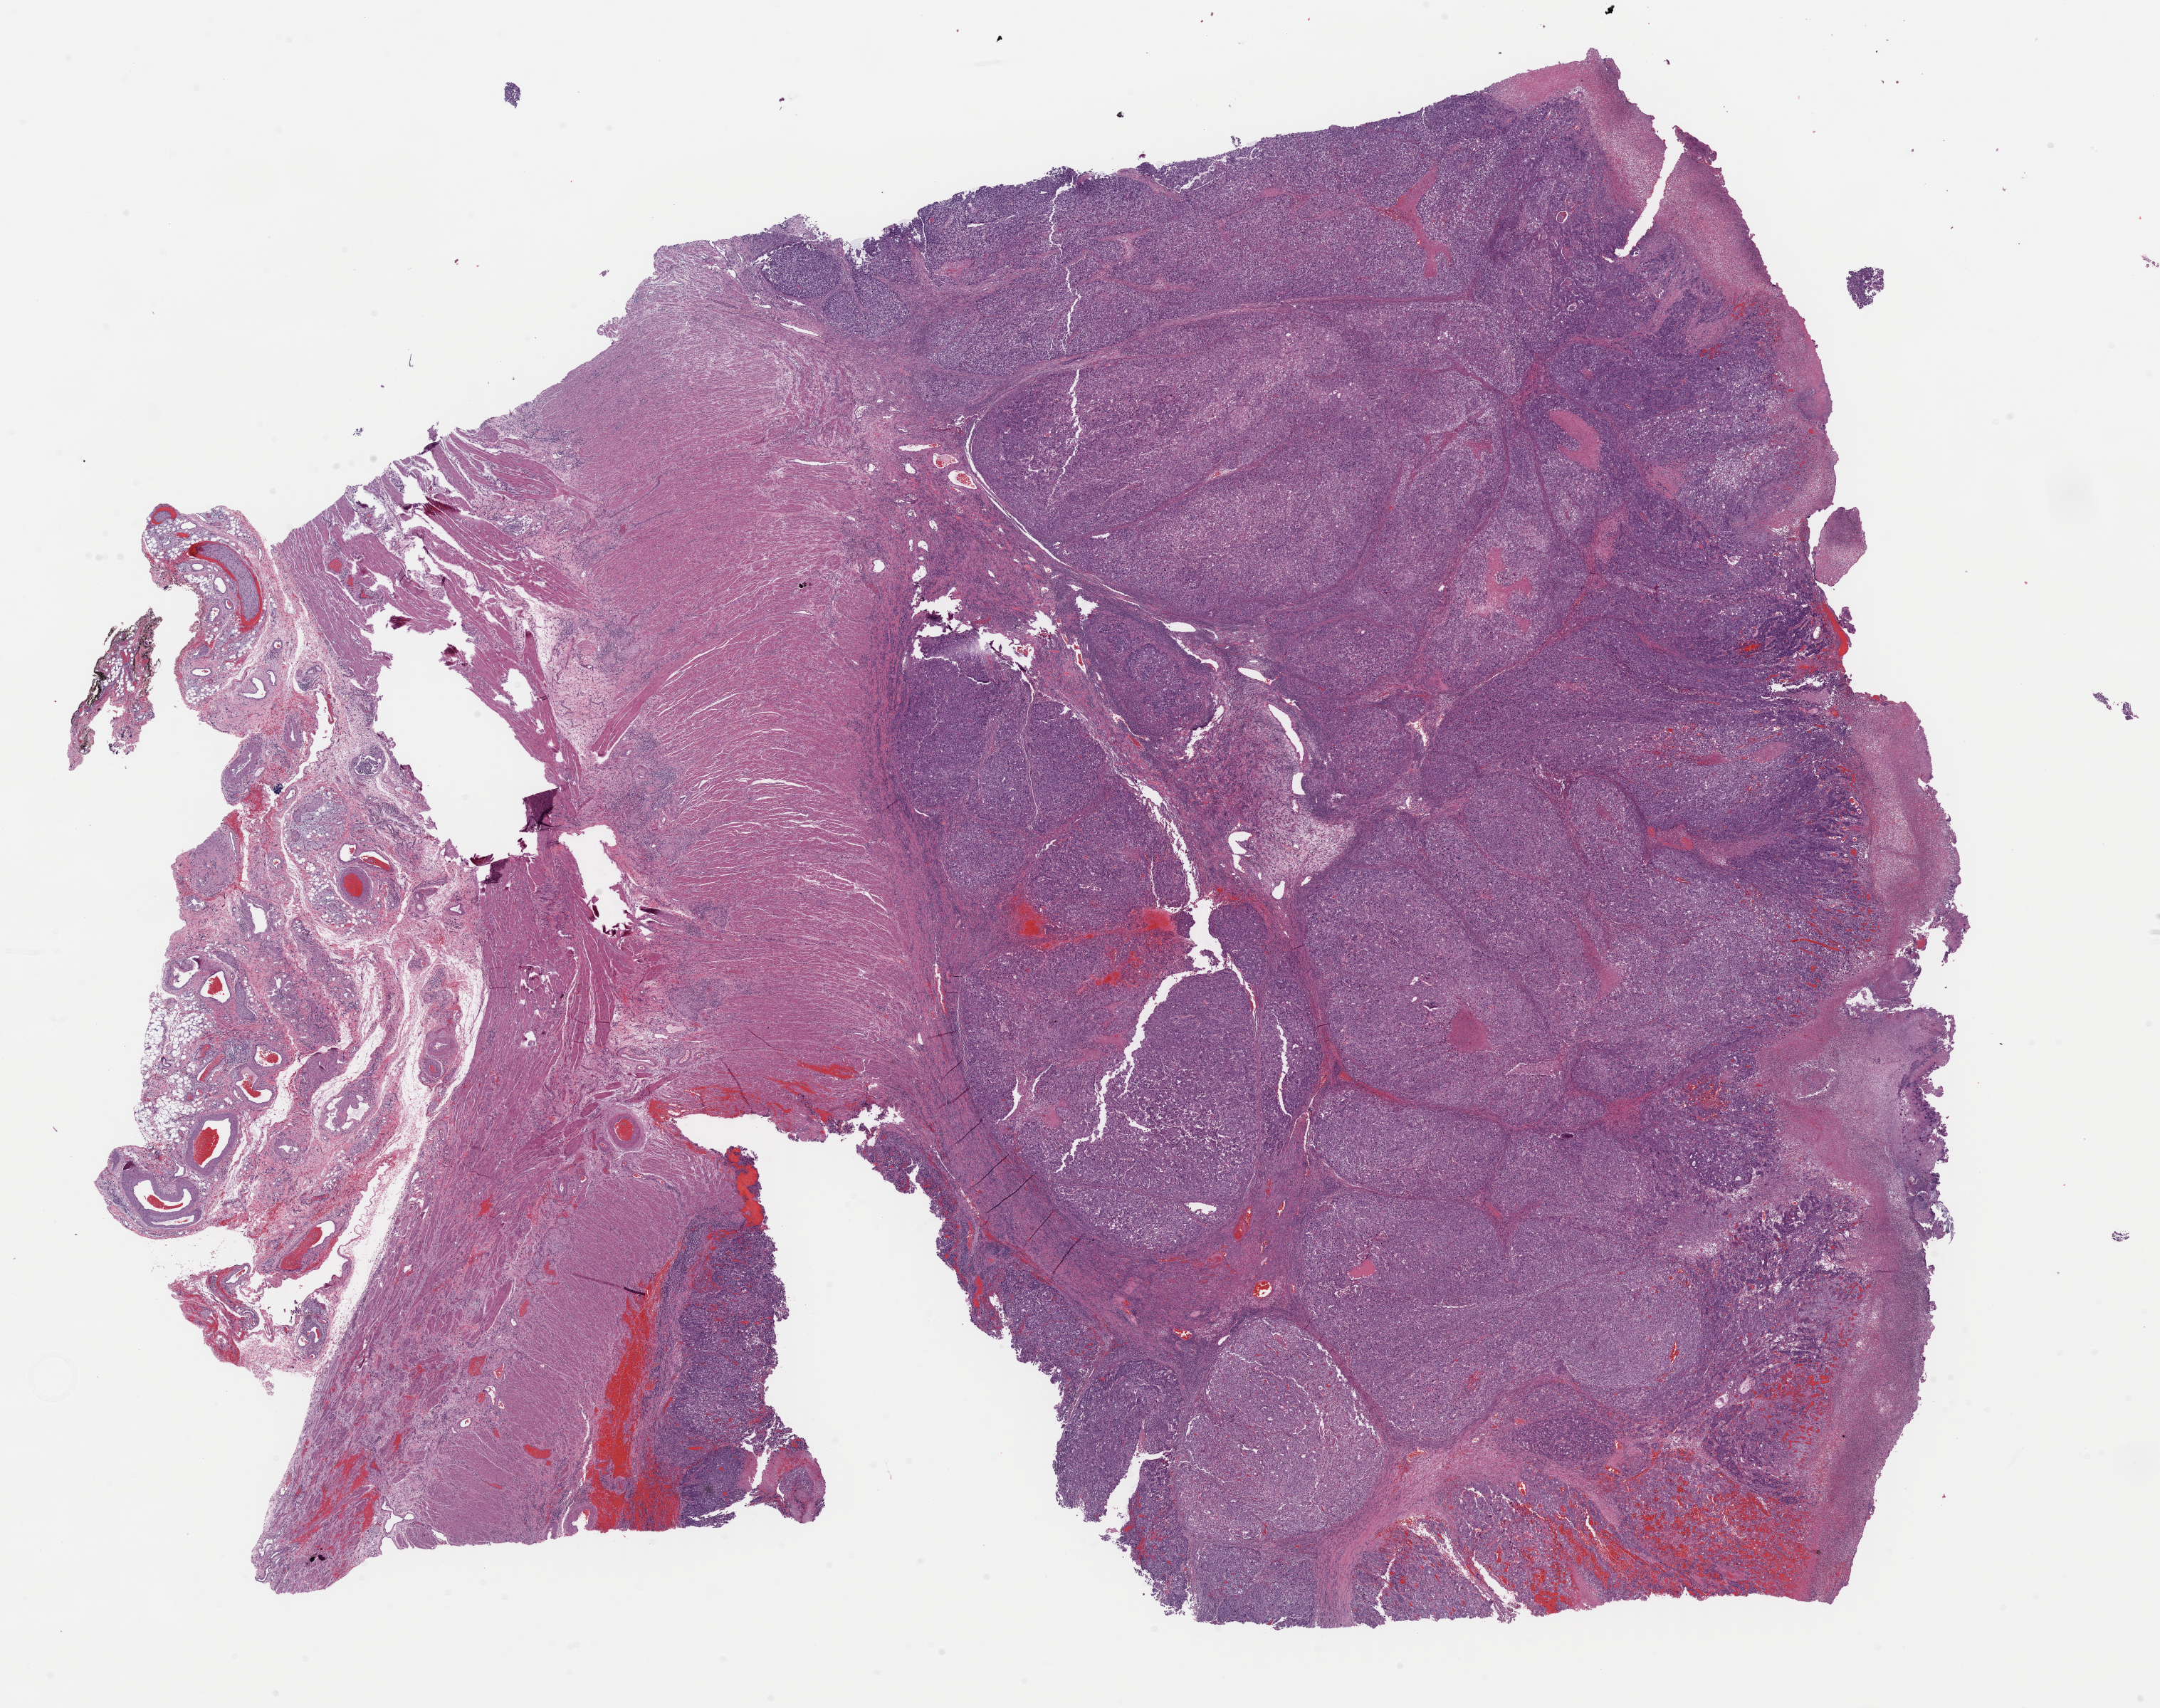
Whole-slide histology image, H&E, whole scanned area (about 23.9 x 18.9 mm, from a 40x scan) shown as a low-resolution overview; formalin-fixed paraffin-embedded (FFPE) diagnostic section; primary tumour sample from the esophagus. Patient sex: female. Histologic grade: G3 (poorly differentiated).
Diagnosis: Adenocarcinoma, NOS (lower third of esophagus). AJCC pathologic stage: IIB (7th edition).